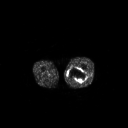
FDG PET of an extremity soft-tissue mass (from a PET/CT study), one axial slice; slice 224 of 267 in the series (ordered by position); 3.27 mm slice thickness; 128 × 128 image matrix, field of view 700 × 700 mm. Patient: male, 44 years. Case-level facts recorded for this patient, not image findings: histological type: undifferentiated pleomorphic liposarcoma; grade: high; site of the primary tumour: left thigh.
Outlined on this slice (expert contour drawn on MRI and transferred to this co-registered scan by the dataset authors):
- gross tumour volume including surrounding oedema: bounding box <67,67,87,83> (left, top, right, bottom; pixels)
- gross tumour volume (mass): <68,67,87,83>